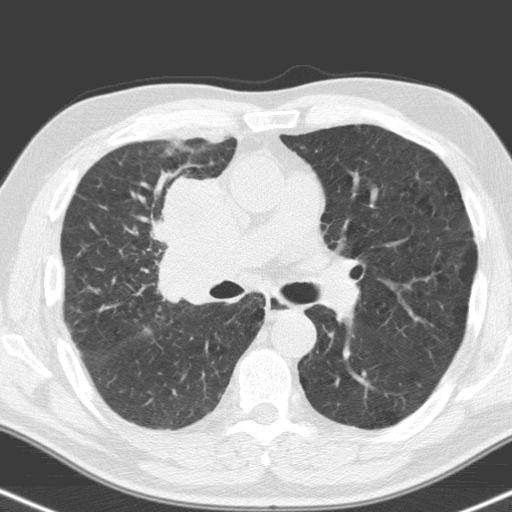
Low-dose screening chest CT, one axial slice; slice 96 of 160 in the series (ordered by position); lung window (W 1500 / L -600 HU); 3.2 mm slice thickness; 512 × 512 image matrix, field of view 324 × 324 mm.
Annotated regions visible in this slice (outlined manually by an expert reader):
- lesion 1 (tumor, hilum of right lung): bounding box (x1, y1, x2, y2) in pixels: (161, 179, 251, 303)